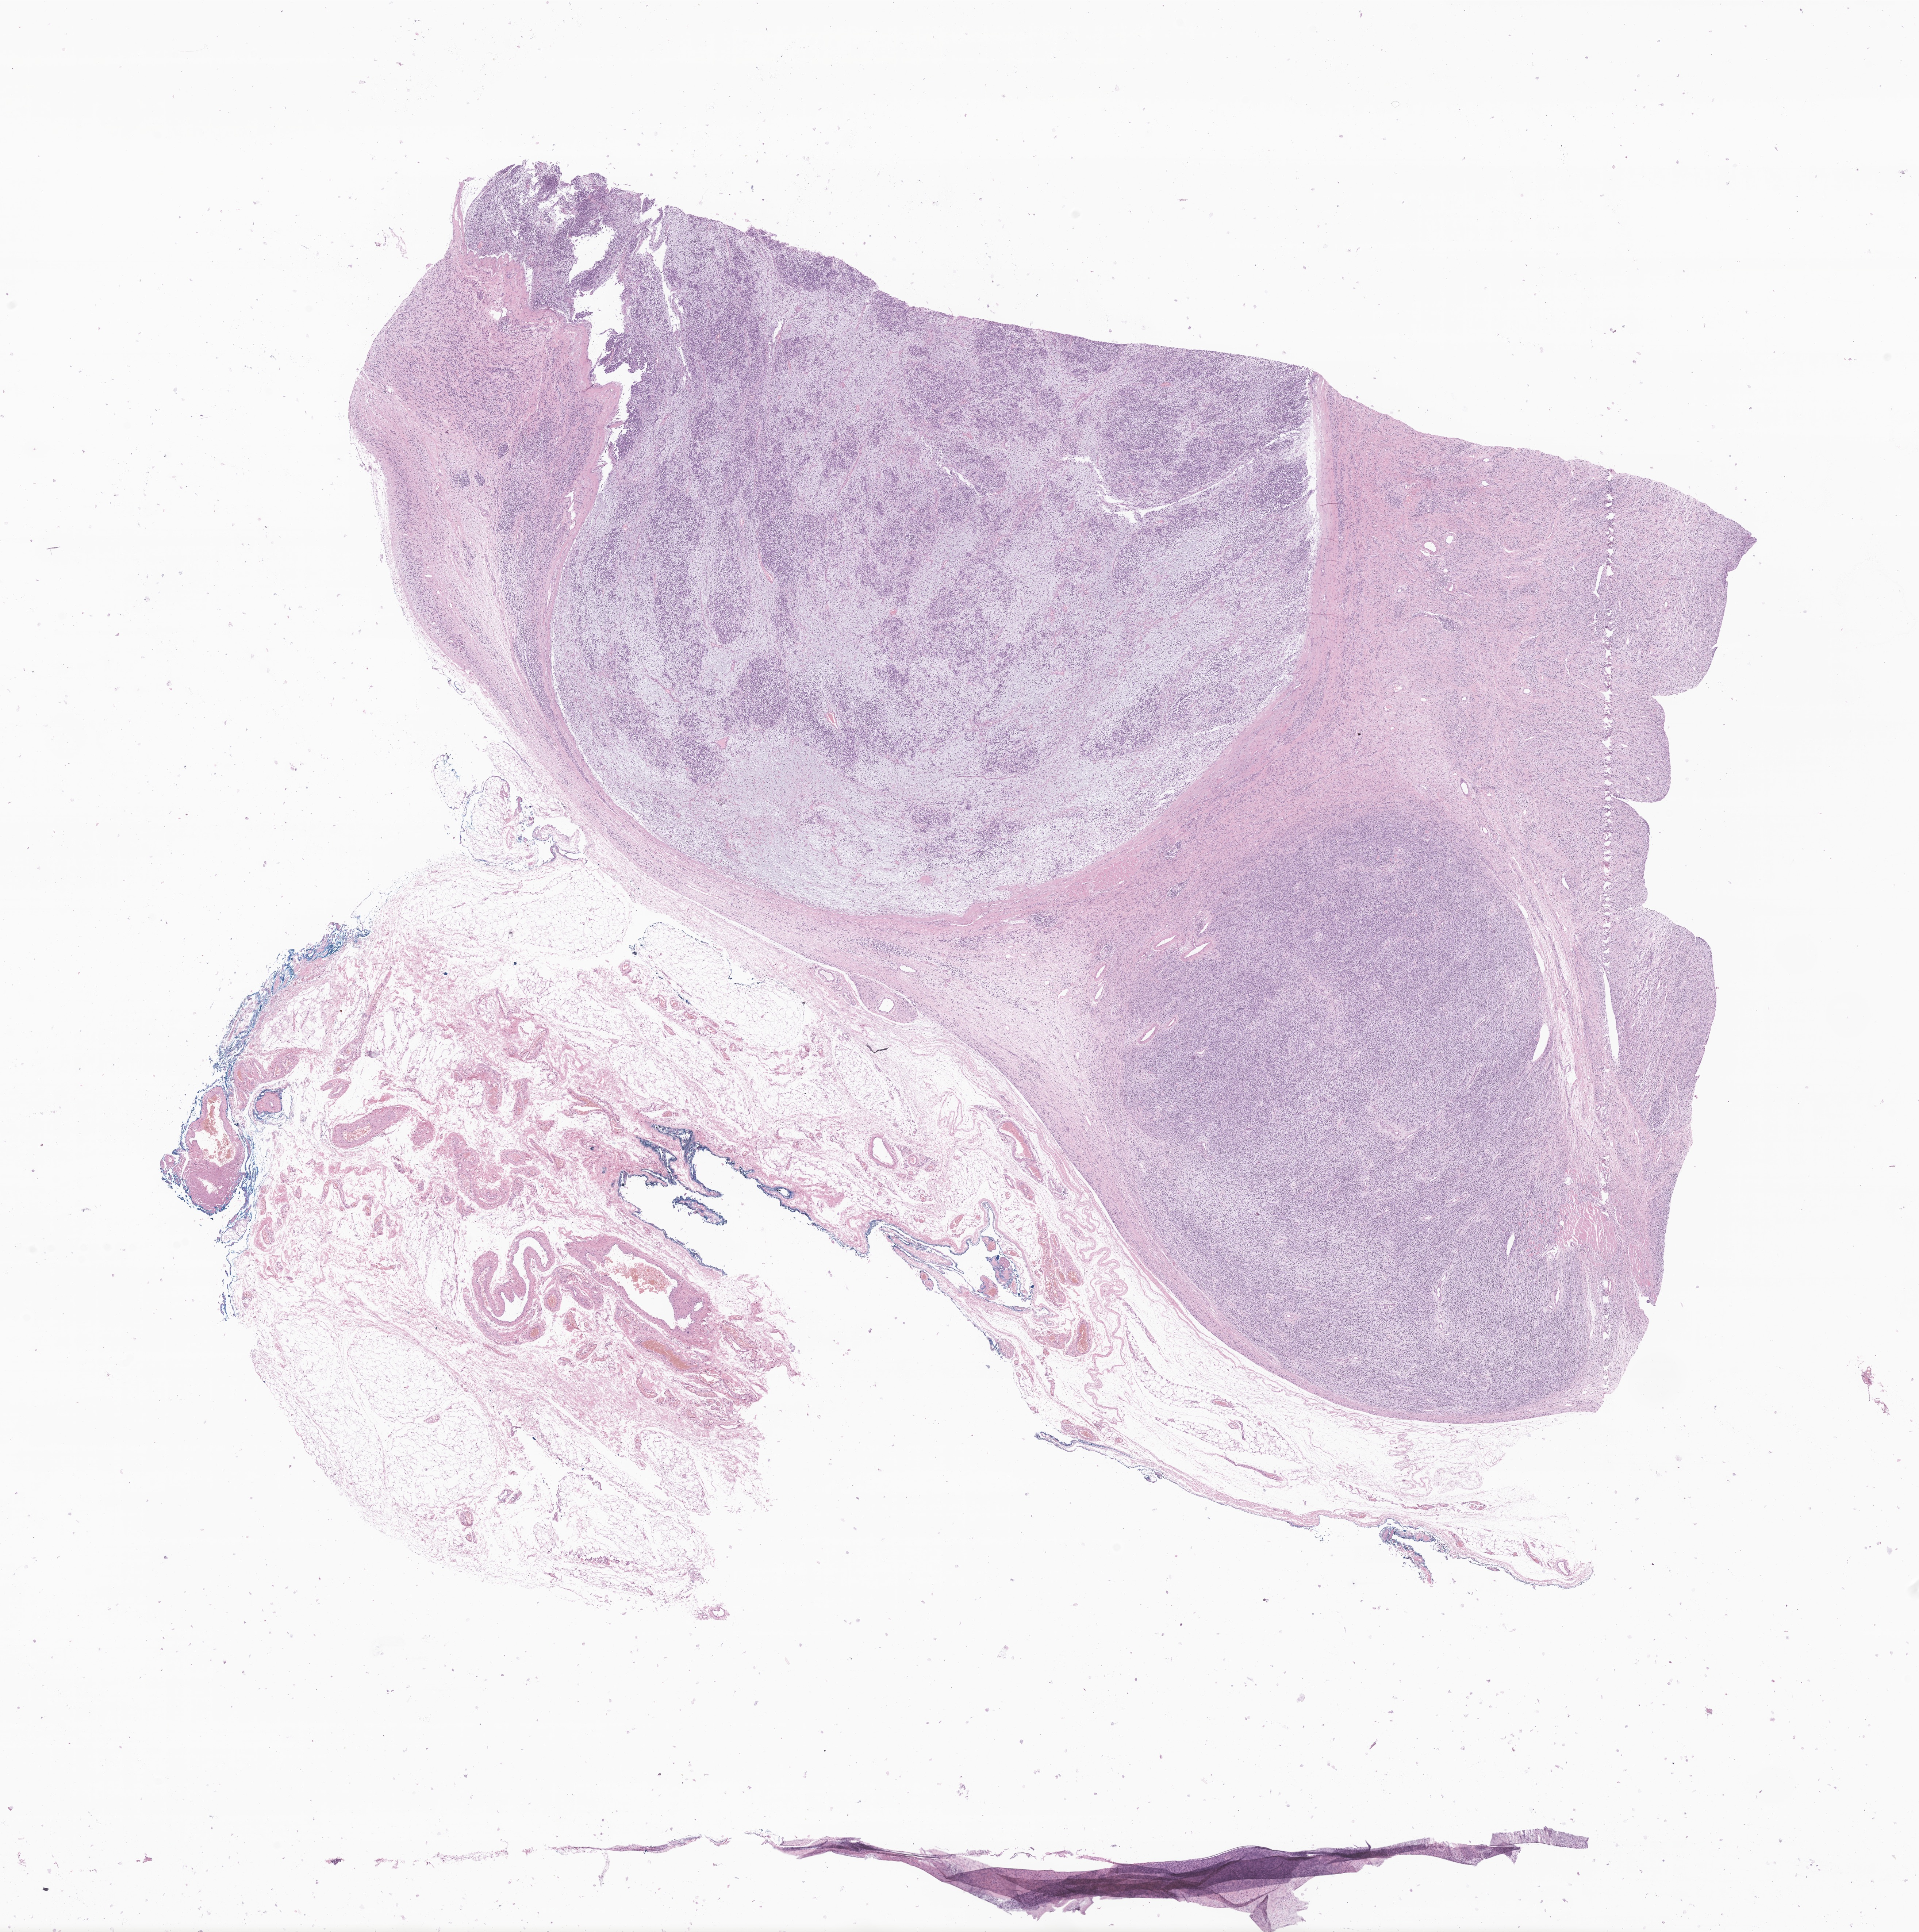
Hematoxylin and eosin (H&E) whole-slide image of tumor tissue from the testis, low-resolution overview of the scanned area, about 22.2 x 22.3 mm, formalin-fixed paraffin-embedded section. Patient male; age 69 months (5 years 9 months).
Diagnosis (ICD-O-3 morphology term): Embryonal rhabdomyosarcoma, NOS.